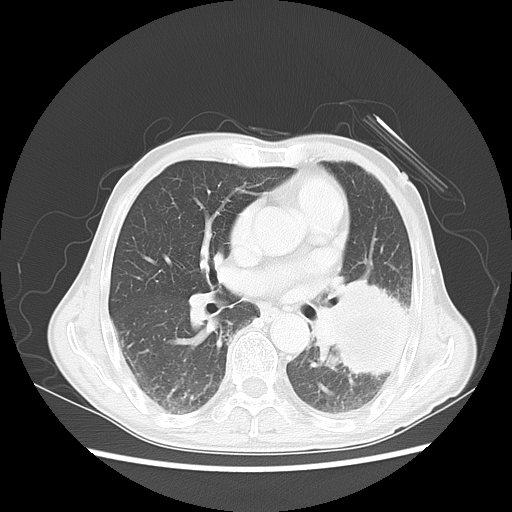
Chest CT, one axial slice. Slice 26 of 51 in the series (ordered by position). Reconstruction kernel LUNG. 120 kVp. Lung window (W 1500 / L -600 HU). 5 mm slice thickness. 512 × 512 image matrix, field of view 360 × 360 mm. Patient: male, 64 years. From the clinical record (not read from this slice): clinical TNM (as recorded): T4 N0 M0; histopathological grade: G2-3.
Outlined on this slice (bounding box drawn by a radiologist):
- lung tumour (recorded histology: squamous cell carcinoma): bounding box <300,281,408,387> (left, top, right, bottom; pixels)